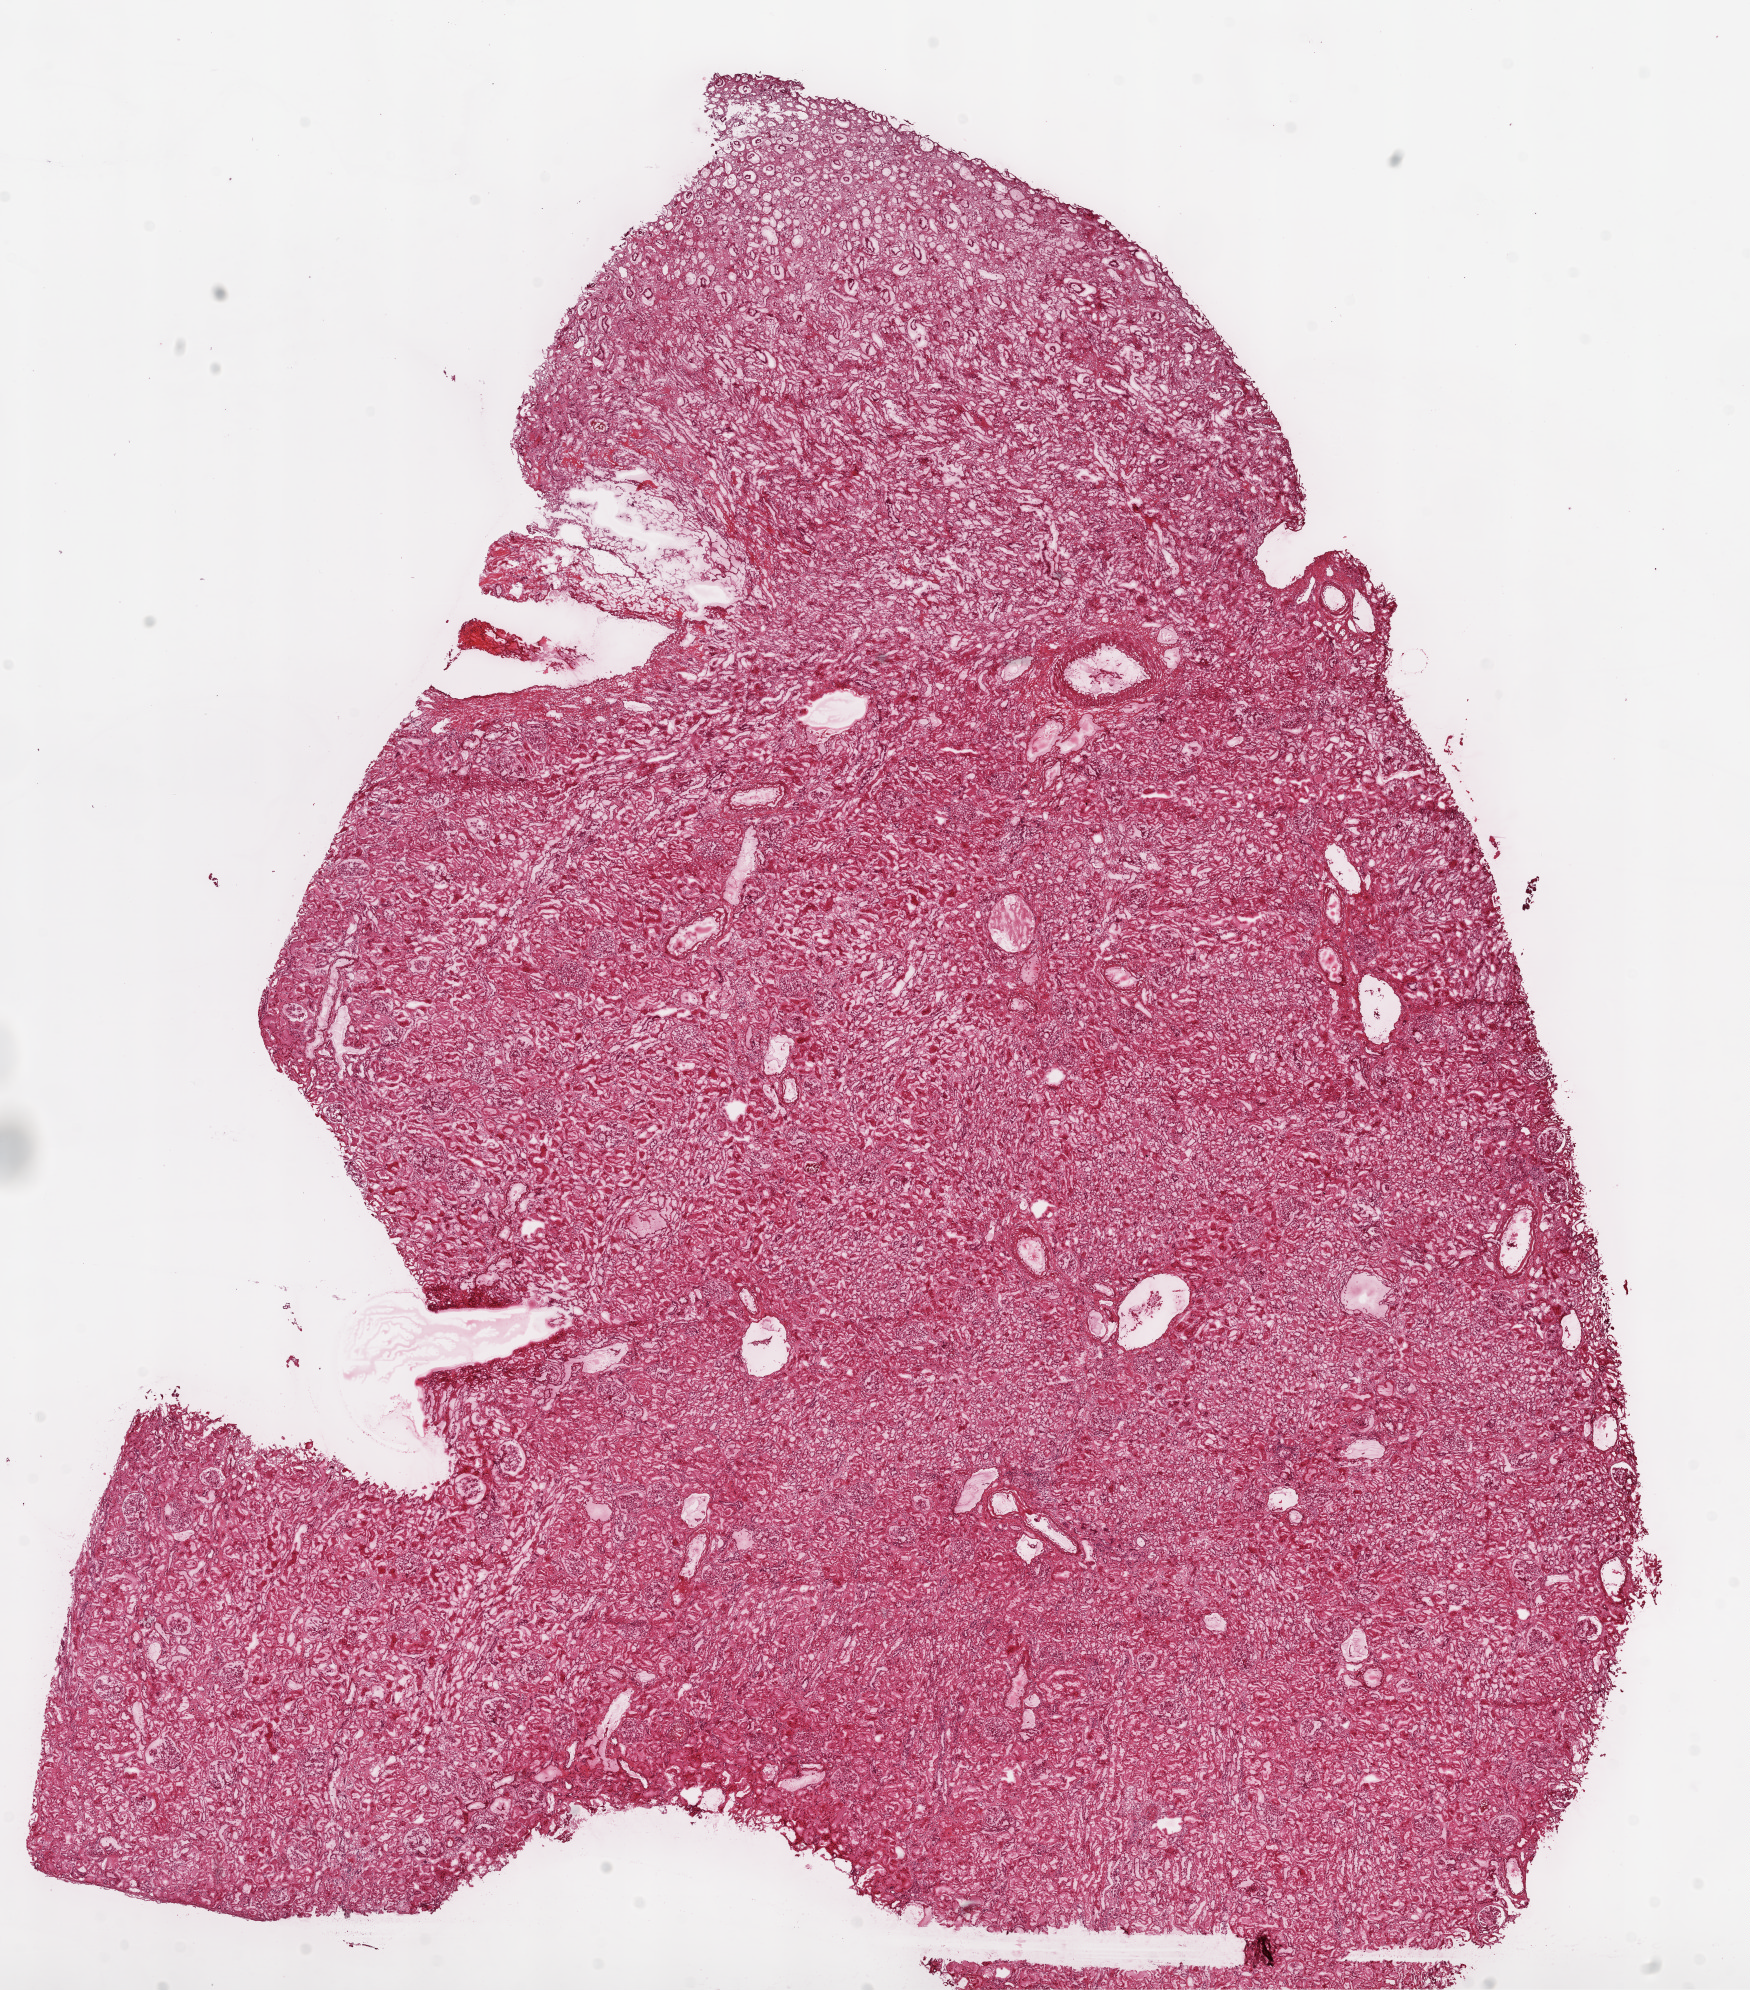
Whole-slide histology image, H&E-stained, a low-resolution overview of the entire scanned area, about 14.0 x 16.0 mm; frozen section from the top of the tissue portion; sample: solid tissue normal (non-tumour tissue), kidney. Female patient; age at initial diagnosis 51 years.
This section: solid tissue normal sample (biorepository sample class). Patient diagnosis: Clear cell adenocarcinoma, NOS.